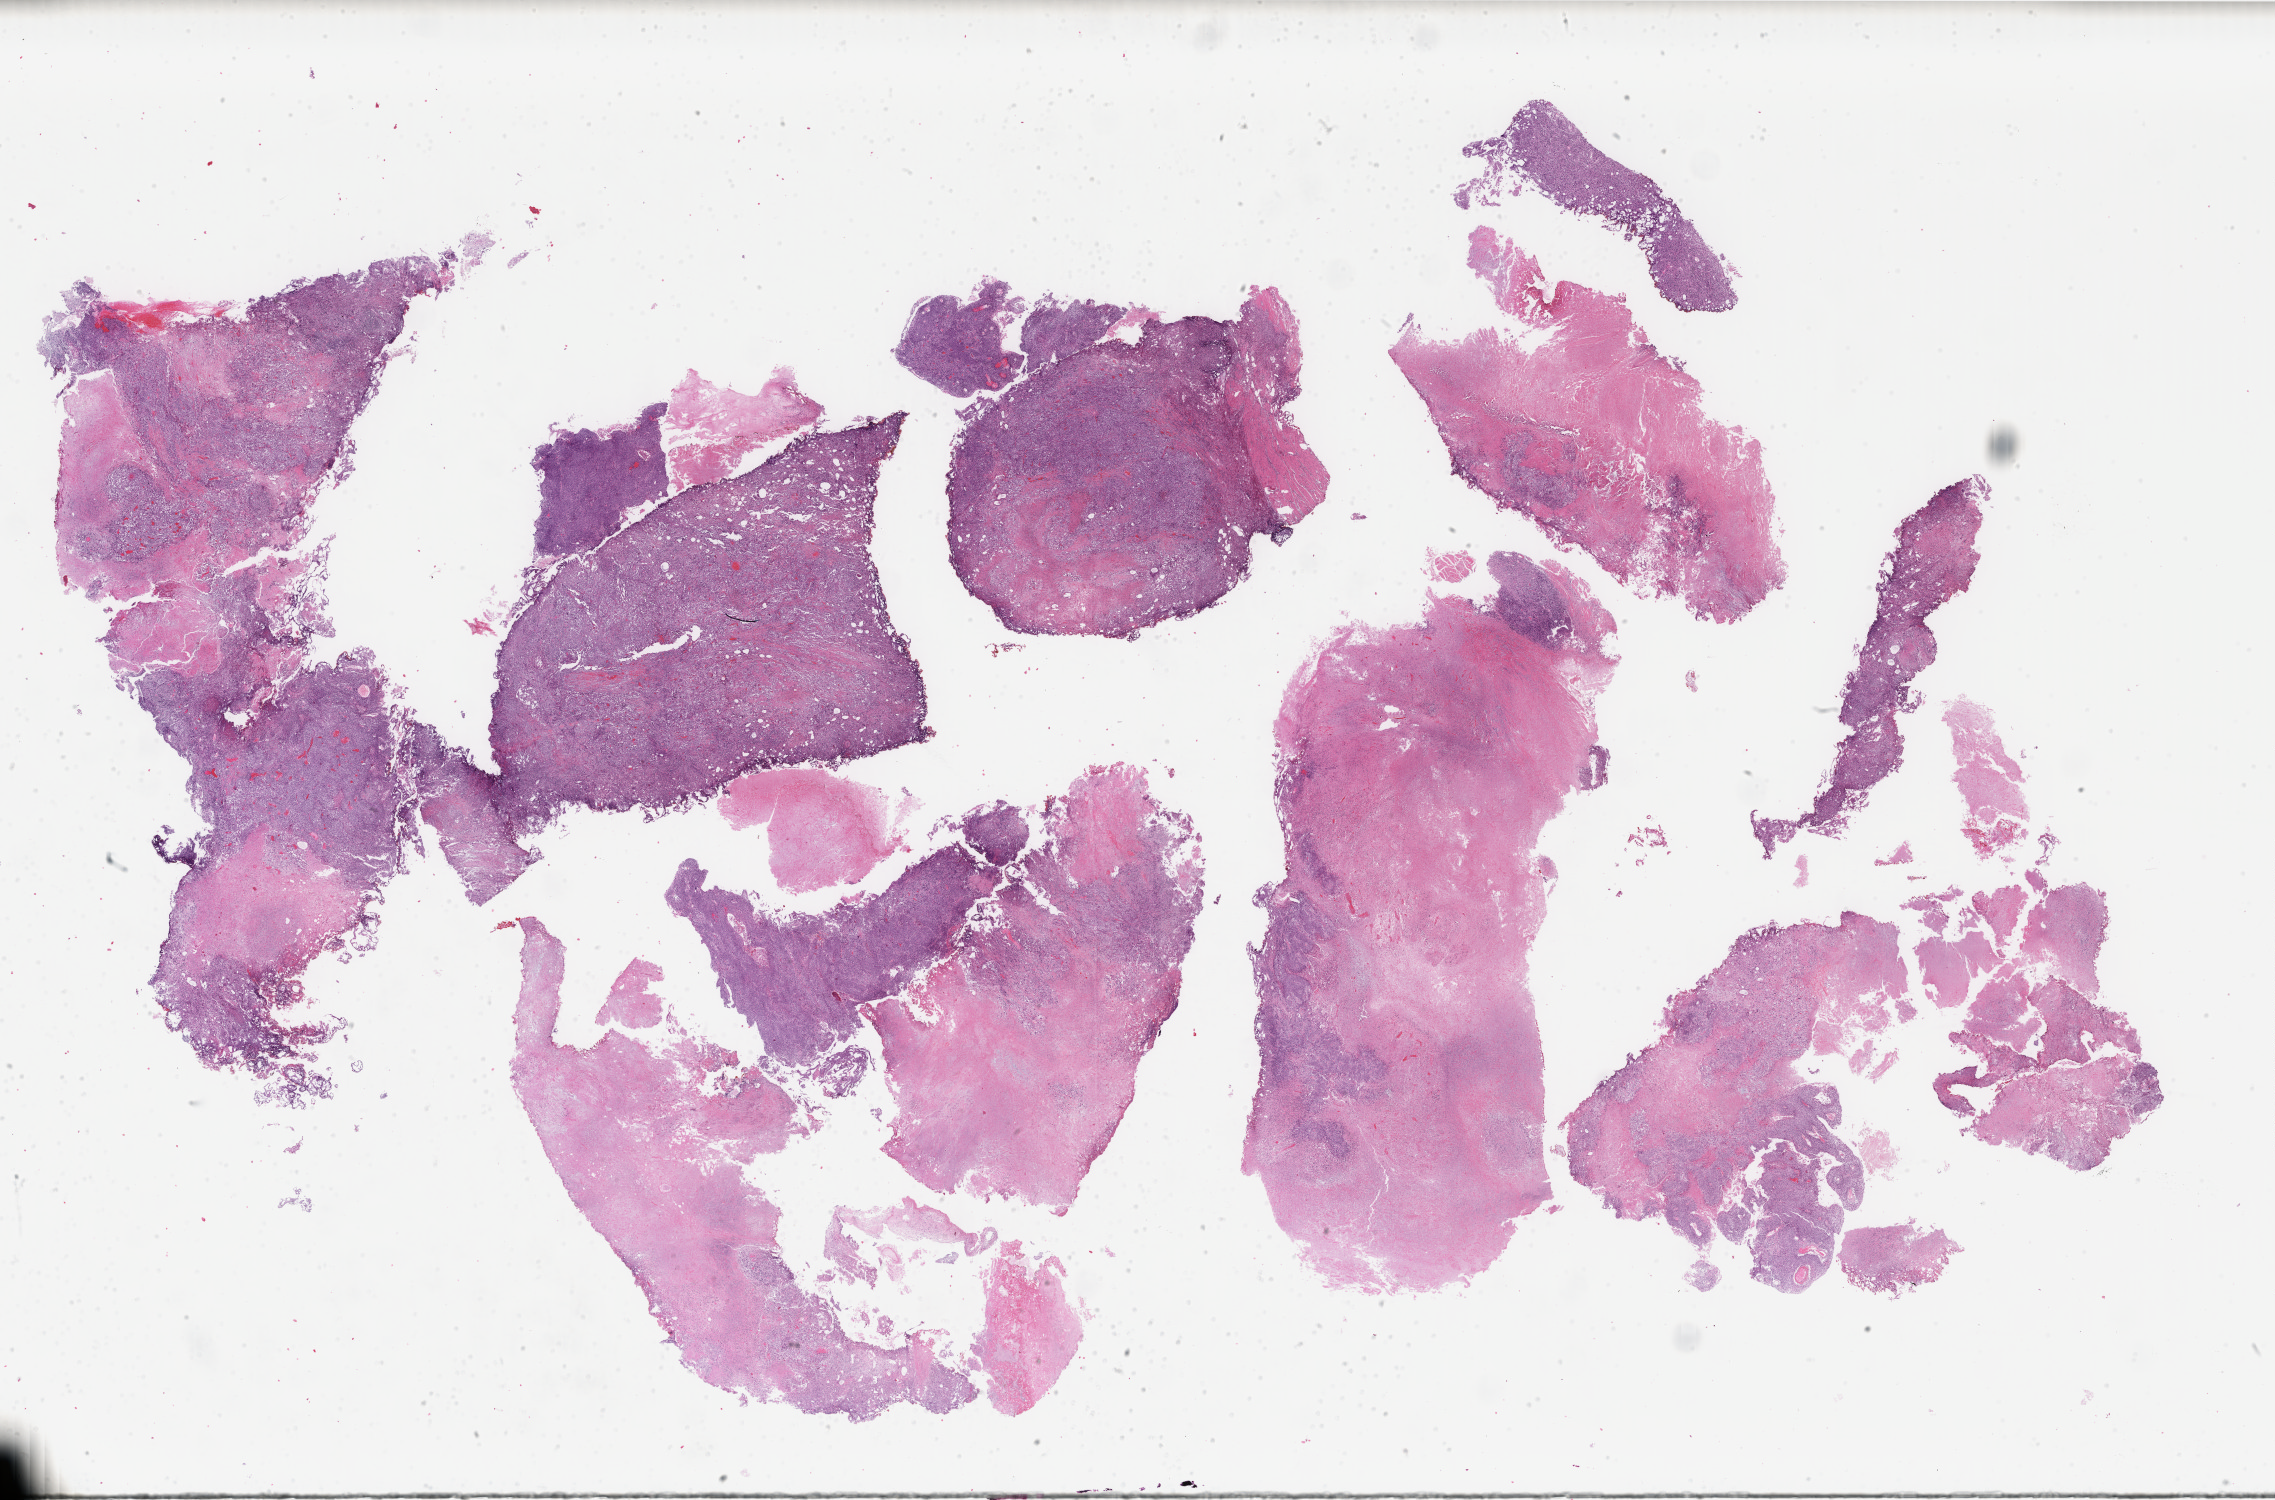
Digitized H&E-stained tissue section (whole slide) — a low-resolution overview of the entire scanned area, about 36.1 x 23.8 mm (from a 40x scan). FFPE section. Bladder, primary tumour sample. Male patient; age at initial diagnosis 50 years.
Diagnosis: Transitional cell carcinoma.